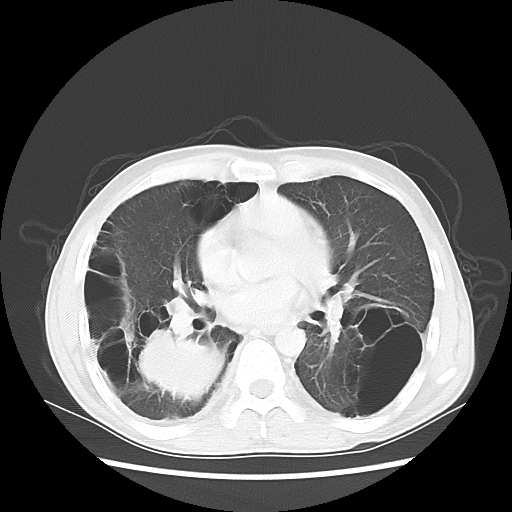
Chest CT, one axial slice. Slice 27 of 57 in the series (ordered by position). Reconstruction kernel LUNG. 140 kVp. Lung window (W 1500 / L -600 HU). 5 mm slice thickness. 512 × 512 image matrix, field of view 351 × 351 mm. Patient: male, 41 years. From the clinical record (not read from this slice): clinical TNM (as recorded): T4 N0 M1a; histopathological grade: G3.
Structures marked on this image (bounding box drawn by a radiologist):
- lung tumour (recorded histology: large cell carcinoma): box from (x=116, y=315) to (x=227, y=410) px